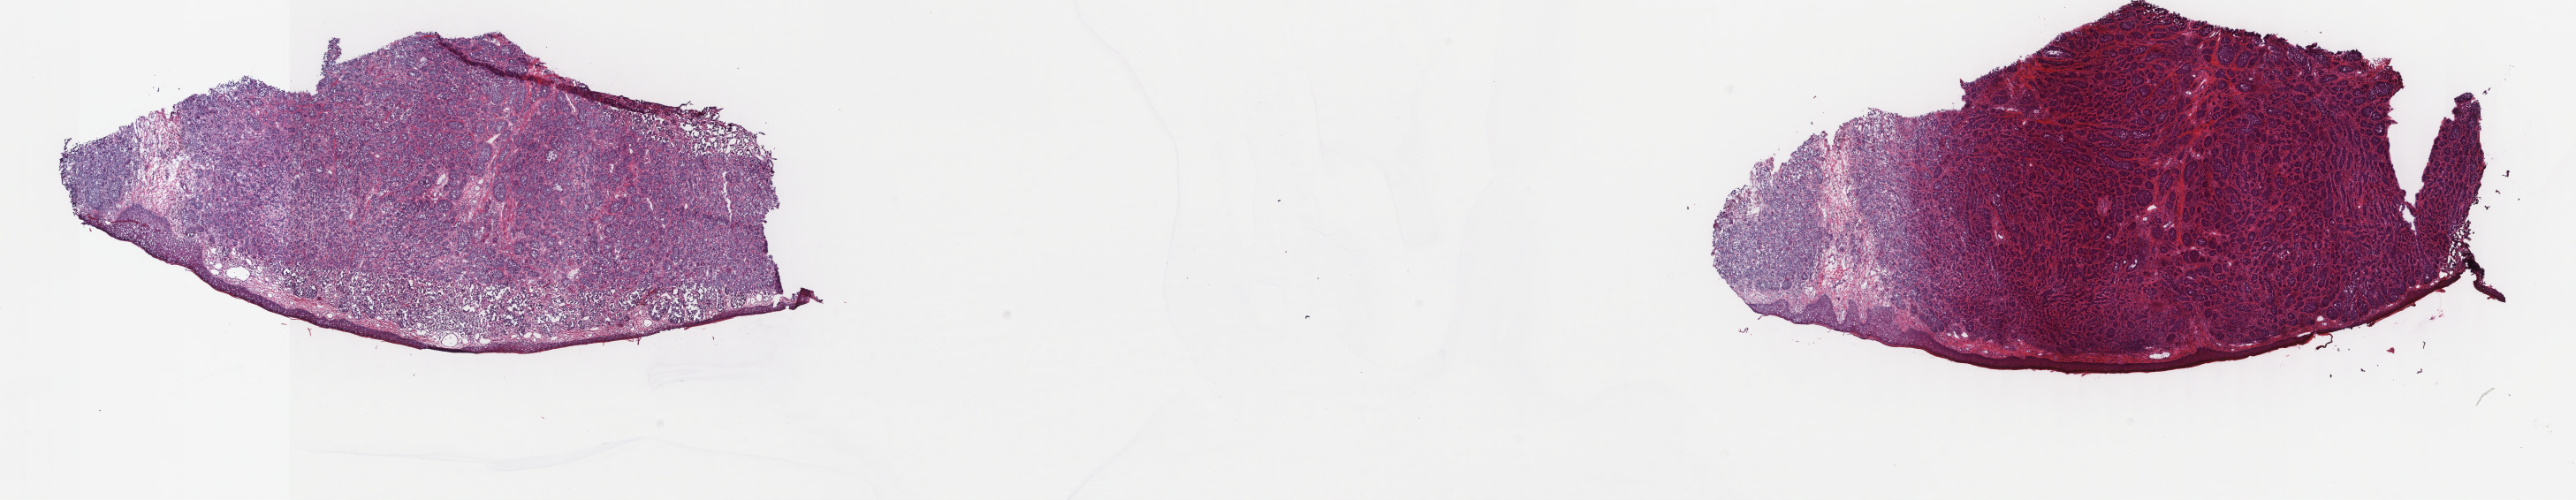
Whole-slide histology image, H&E-stained — low-resolution overview of the scanned area, about 23.1 x 4.5 mm; frozen section; metastatic tumour sample, sampled site not recorded. Male patient; age at initial diagnosis 81 years. Composition of this section per pathologist review: tumour cells 95%, tumour nuclei 95%, normal cells 5%, stromal cells 0%, necrosis 0%. Infiltration values recorded for this section: lymphocyte infiltration 0%, monocyte infiltration 0%, neutrophil infiltration 0%.
• this section: metastatic tumour tissue
• patient diagnosis: Malignant melanoma, NOS